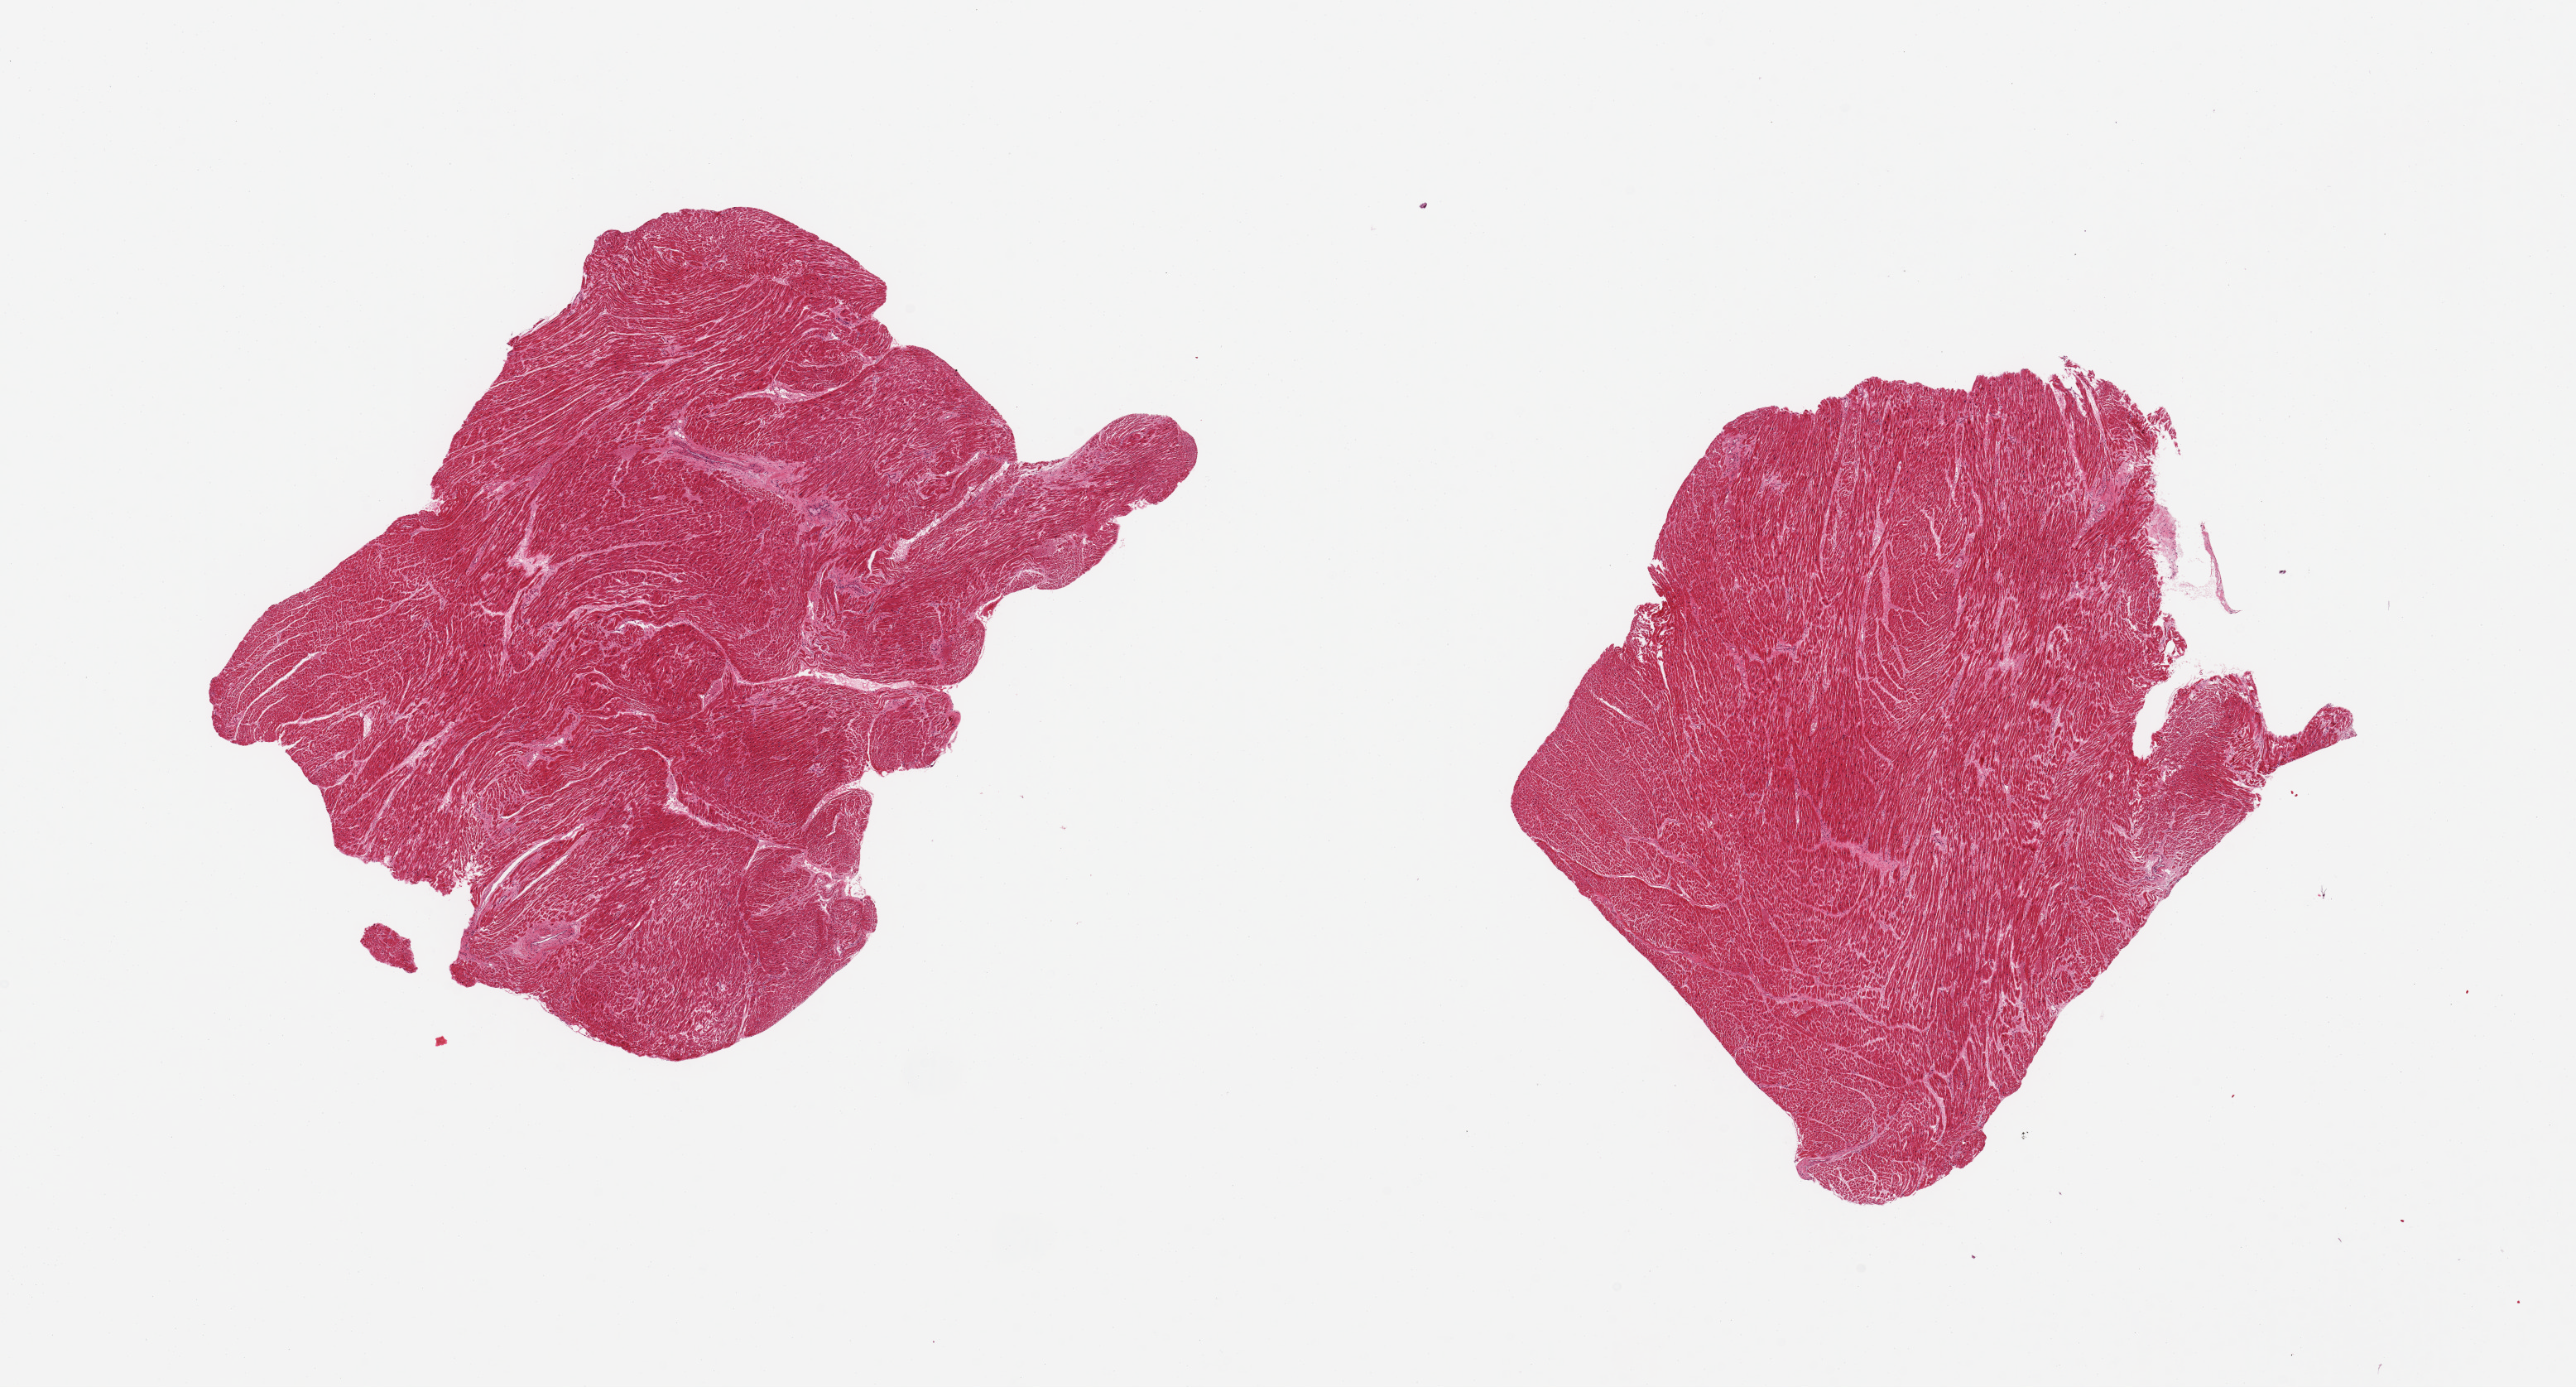
Digitized H&E-stained section, low-resolution overview of the scanned area, about 24.6 x 13.2 mm; PAXgene-fixed, paraffin-embedded tissue; section of heart (target tissue); tissue donor sample. Donor sex: female.
- review note (as recorded): 2 pieces